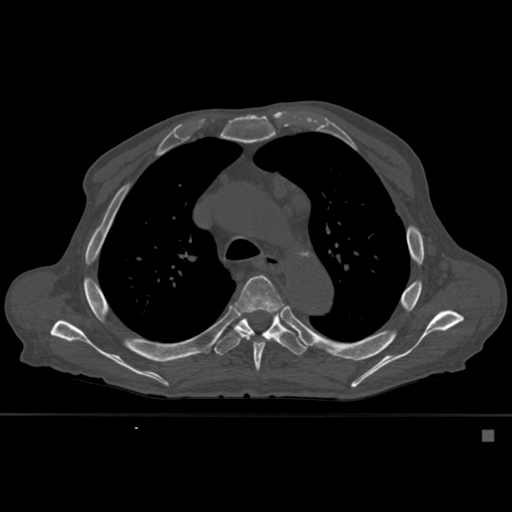
CT including the spine, one axial slice. Position 394 of 527 along the scan axis. Bone window (W 1800 / L 400 HU). 1.5 mm slice thickness. 512 × 512 image matrix, field of view 373 × 373 mm. Male patient, age 78 years. Case-level facts recorded for this patient, not image findings: primary cancer: prostate.
Outlined on this slice (semi-automatically segmented with operator editing):
- T5 vertebra: bounding box <235,275,283,372> (left, top, right, bottom; pixels)
- T6 vertebra: <214,310,306,356>